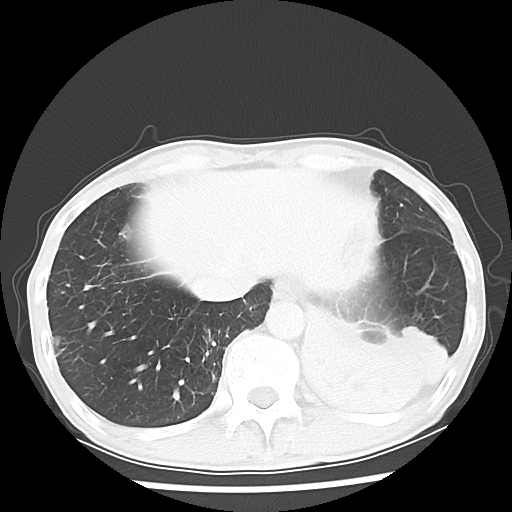
Chest CT, one axial slice. Slice 11 of 64 in the series (ordered by position). 120 kVp. Lung window (W 1500 / L -600 HU). 5 mm slice thickness. 512 × 512 image matrix. Male patient, age 68 years. Case-level facts recorded for this patient, not image findings: clinical TNM (as recorded): T4 N0 M0.
Outlined on this slice (bounding box drawn by a radiologist):
- lung tumour (recorded histology: squamous cell carcinoma): bounding box <300,313,449,420> (left, top, right, bottom; pixels)